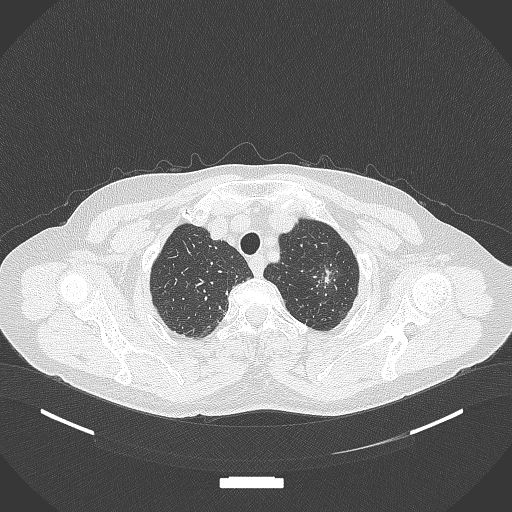
Chest CT, one axial slice; position 315 of 369 along the scan axis; reconstruction kernel B70f; lung window (W 1500 / L -600 HU); 1 mm slice thickness; 512 × 512 image matrix, field of view 400 × 400 mm. Patient: female, 64 years. From the clinical record (not read from this slice): clinical TNM (as recorded): T1c N0 M0; histopathological grade: G1.
Outlined on this slice (bounding box drawn by a radiologist):
- lung tumour (recorded histology: adenocarcinoma): bounding box [x1, y1, x2, y2] px = [318, 263, 335, 289]